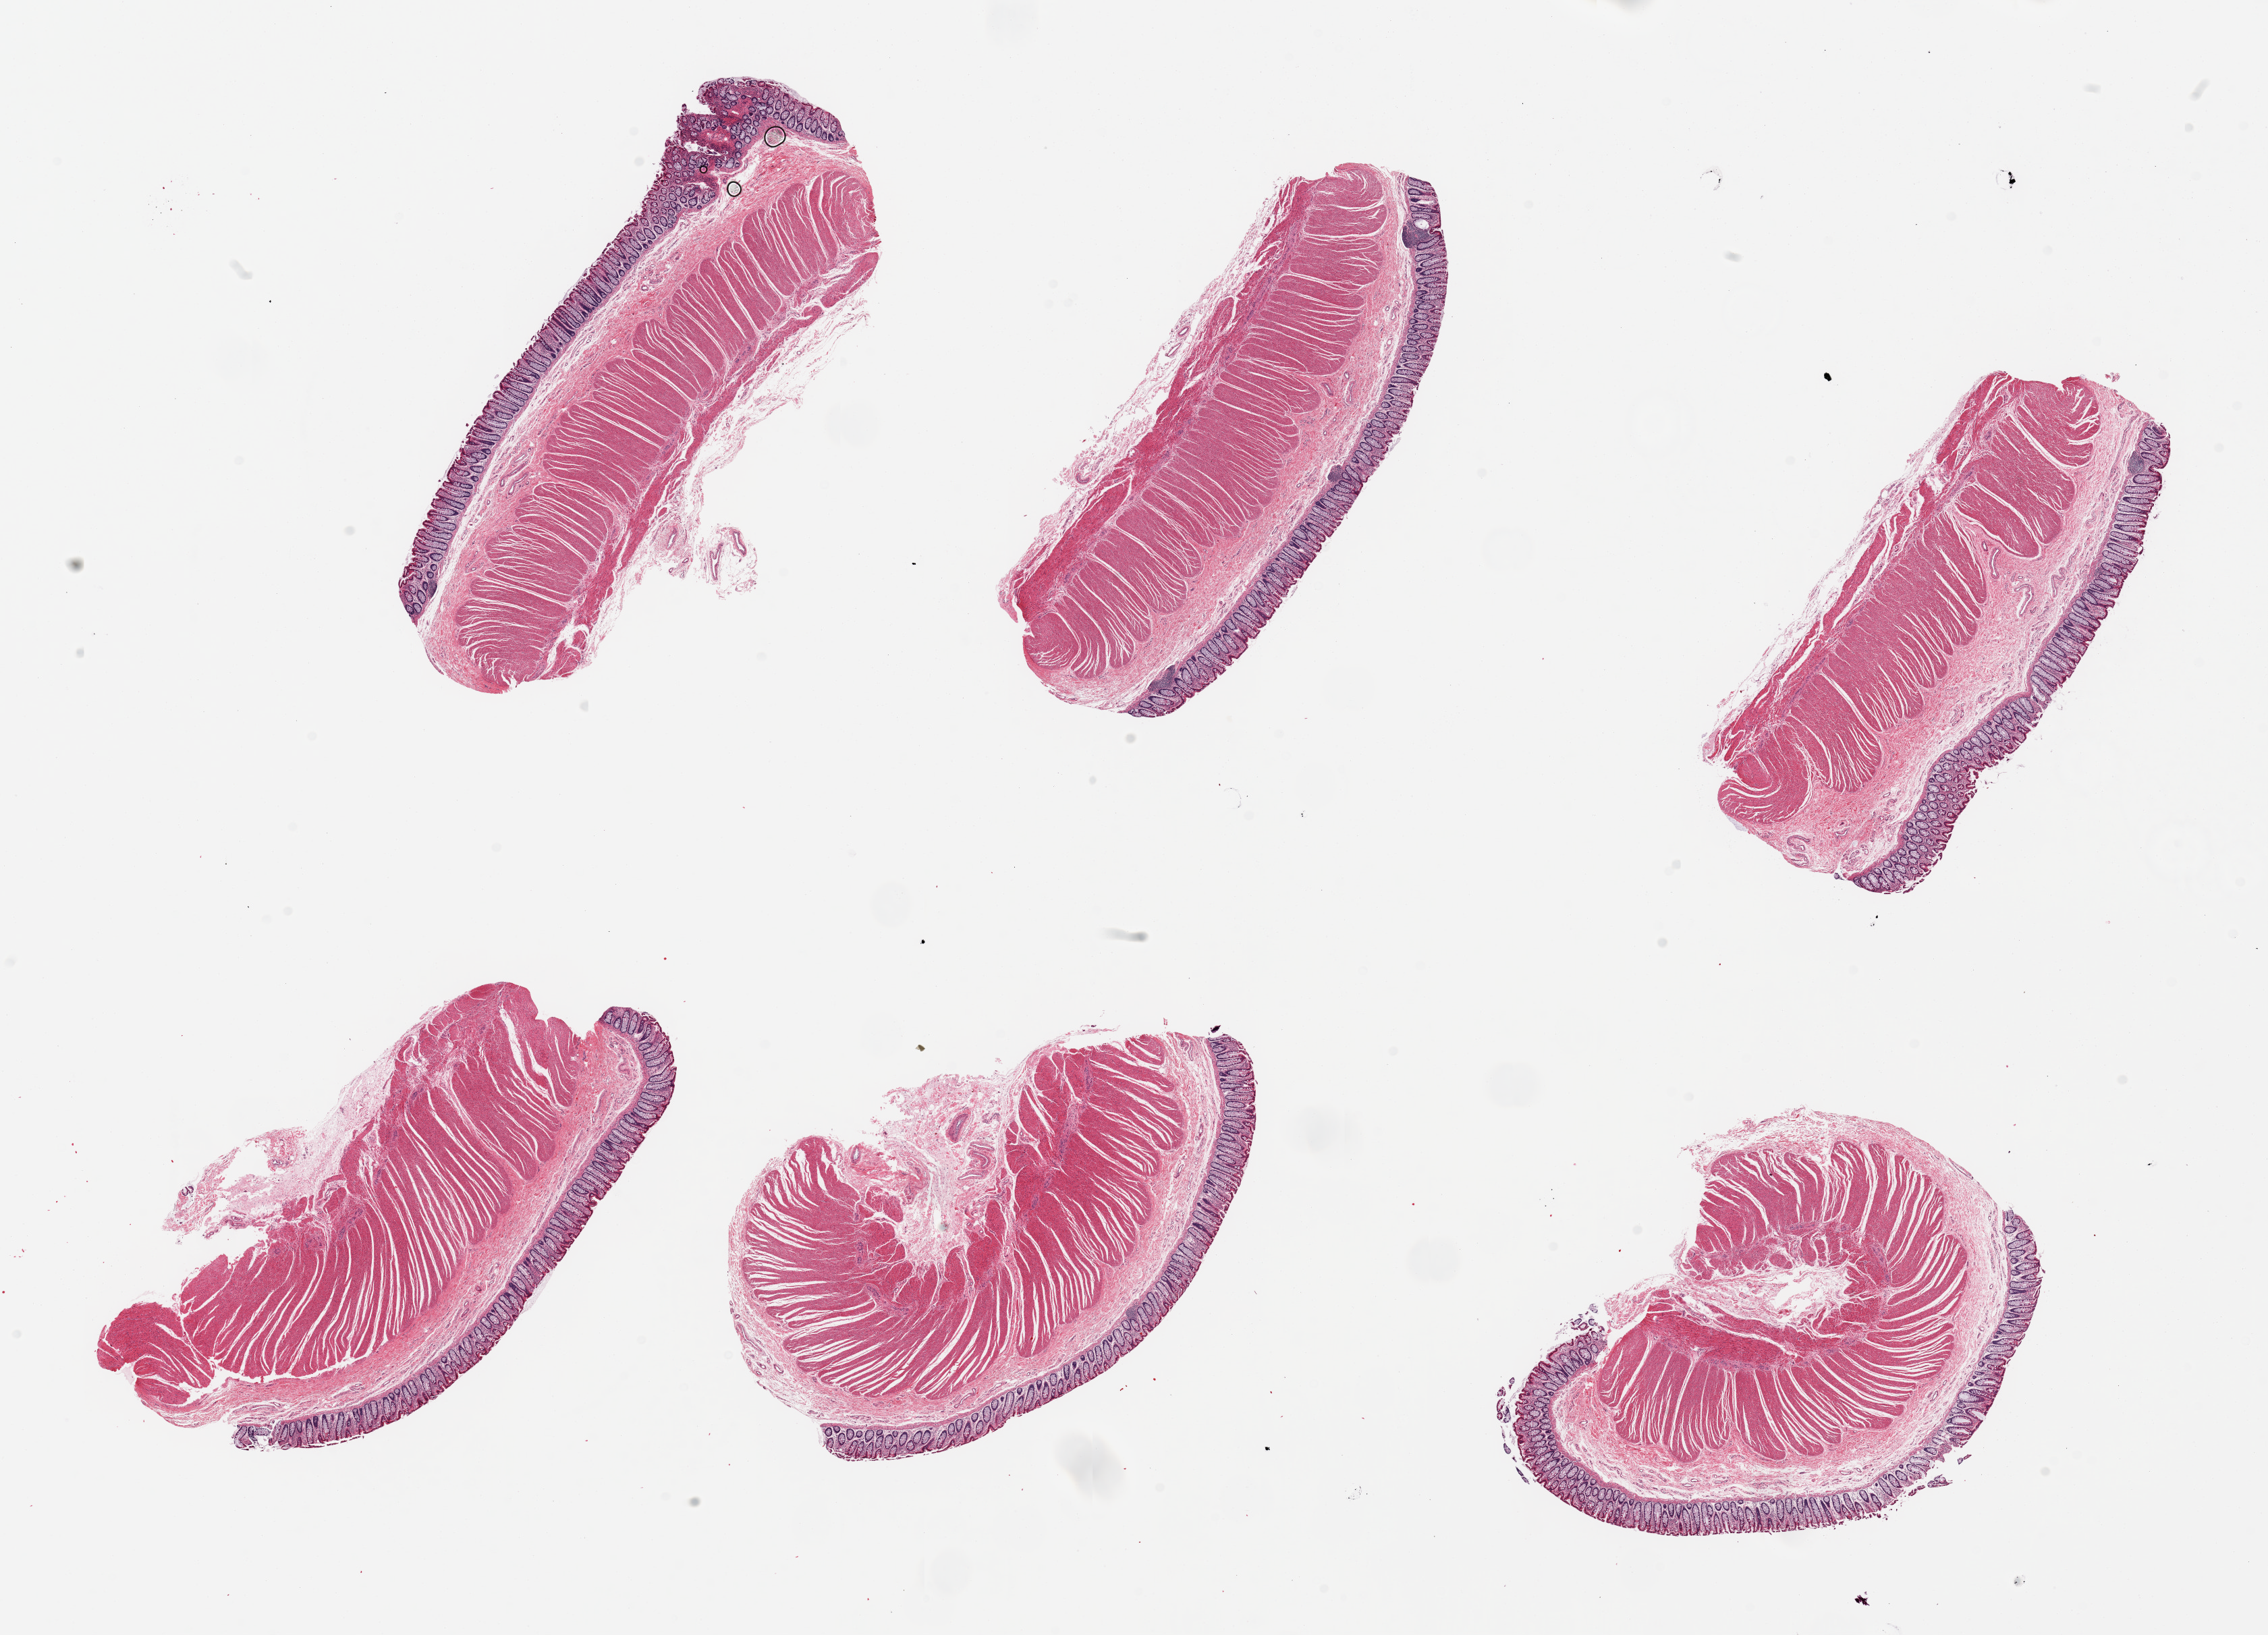
Digitized haematoxylin and eosin-stained section, brightfield, a low-resolution overview of the entire scanned area, about 26.6 x 19.2 mm; PAXgene-fixed, paraffin-embedded tissue; sampled site (target tissue): sigmoid colon; tissue donor sample. Donor: female.
- reviewer comment on this tissue sample: 6 pieces, ~90% muscularis; 'contaminant mucosa up to ~10%